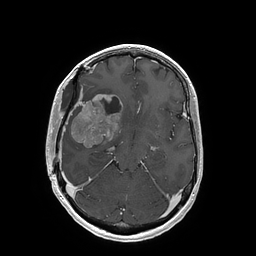
Brain MRI from a brain-tumour surgery series, one axial slice; position 102 of 202 along the scan axis; T1-weighted post-contrast; 1 mm slice thickness; 256 × 256 image matrix. From the clinical record (not read from this slice): histopathology: Glioblastoma; WHO grade: 4; IDH mutation: no.
Structures marked on this image (expert manual segmentation):
- tumour: box from (x=71, y=94) to (x=121, y=148) px